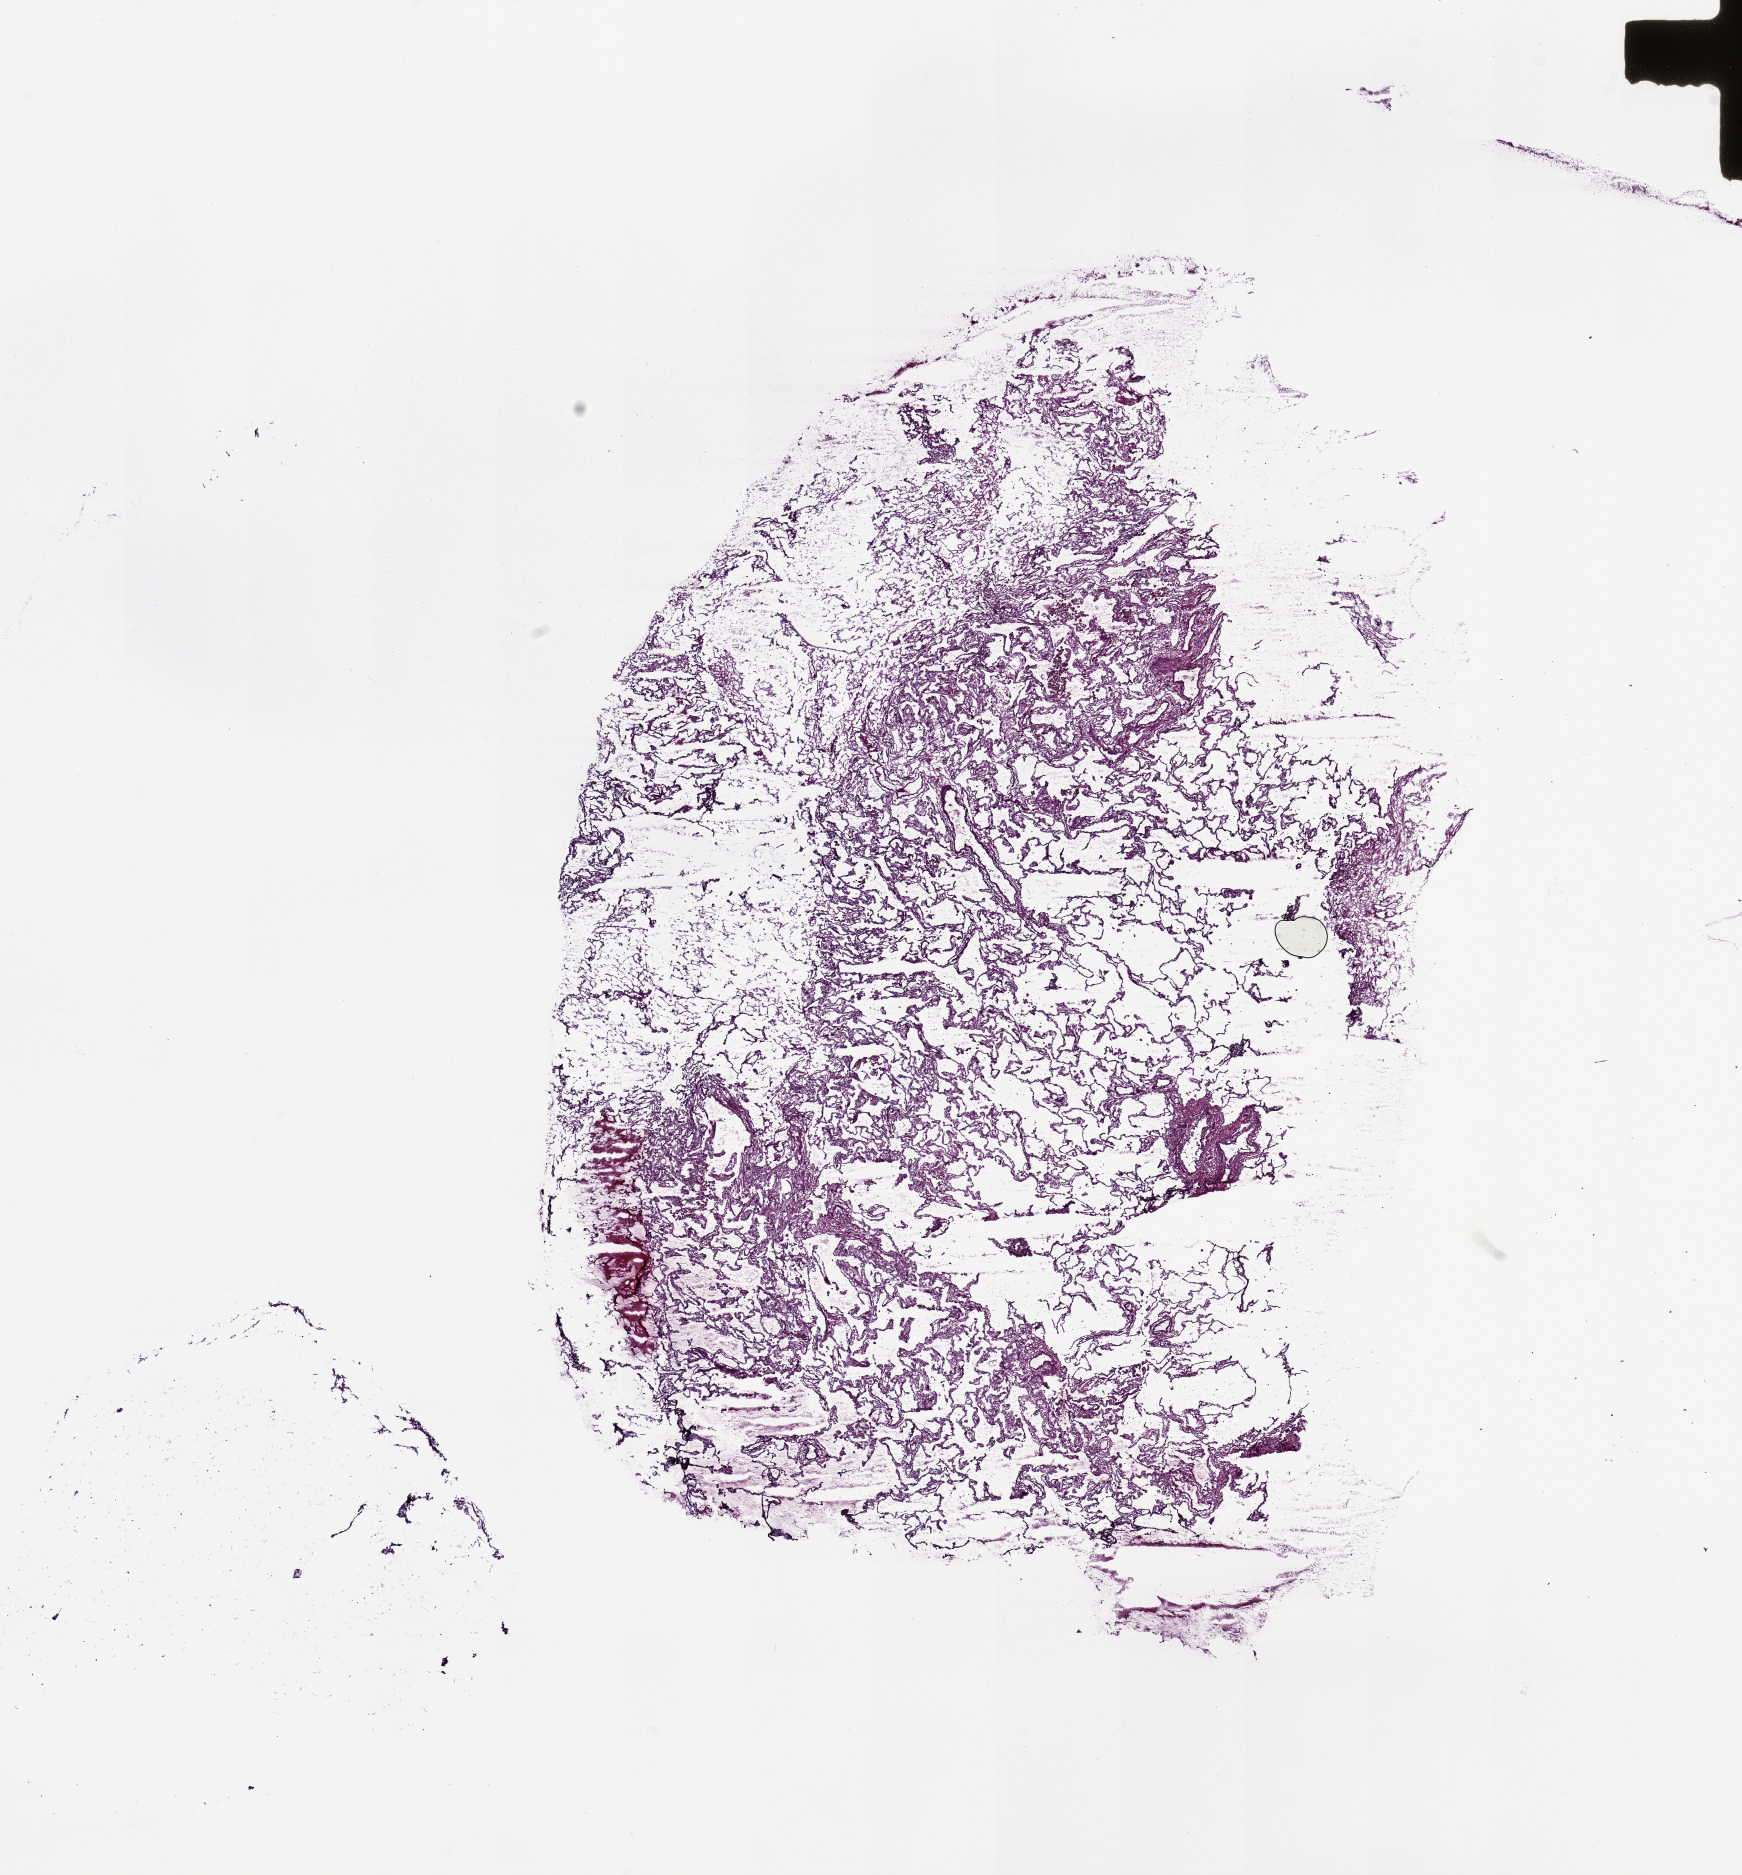
Digitized H&E-stained tissue section (whole slide), low-resolution overview of the scanned area, about 13.8 x 14.8 mm (acquisition: 20x scan). Lung, normal (non-tumour) tissue. Female, 72 y/o.
- this section: normal (non-tumour) tissue from the same patient
- patient diagnosis: Adenocarcinoma, NOS